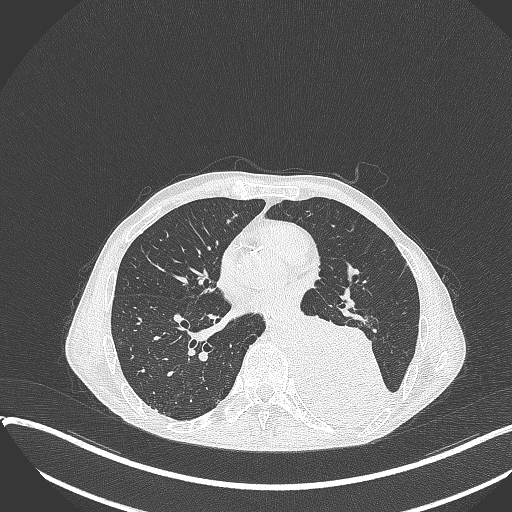
Chest CT, one axial slice; position 162 of 401 along the scan axis; 120 kVp; lung window (W 1500 / L -600 HU); 1 mm slice thickness; 512 × 512 image matrix, field of view 400 × 400 mm. Male patient, age 57 years. Case-level facts recorded for this patient, not image findings: clinical TNM (as recorded): T4 N0 M0.
Annotated regions visible in this slice (rectangle marked by the reading radiologist):
- lung tumour (recorded histology: squamous cell carcinoma): box from (x=290, y=307) to (x=395, y=431) px